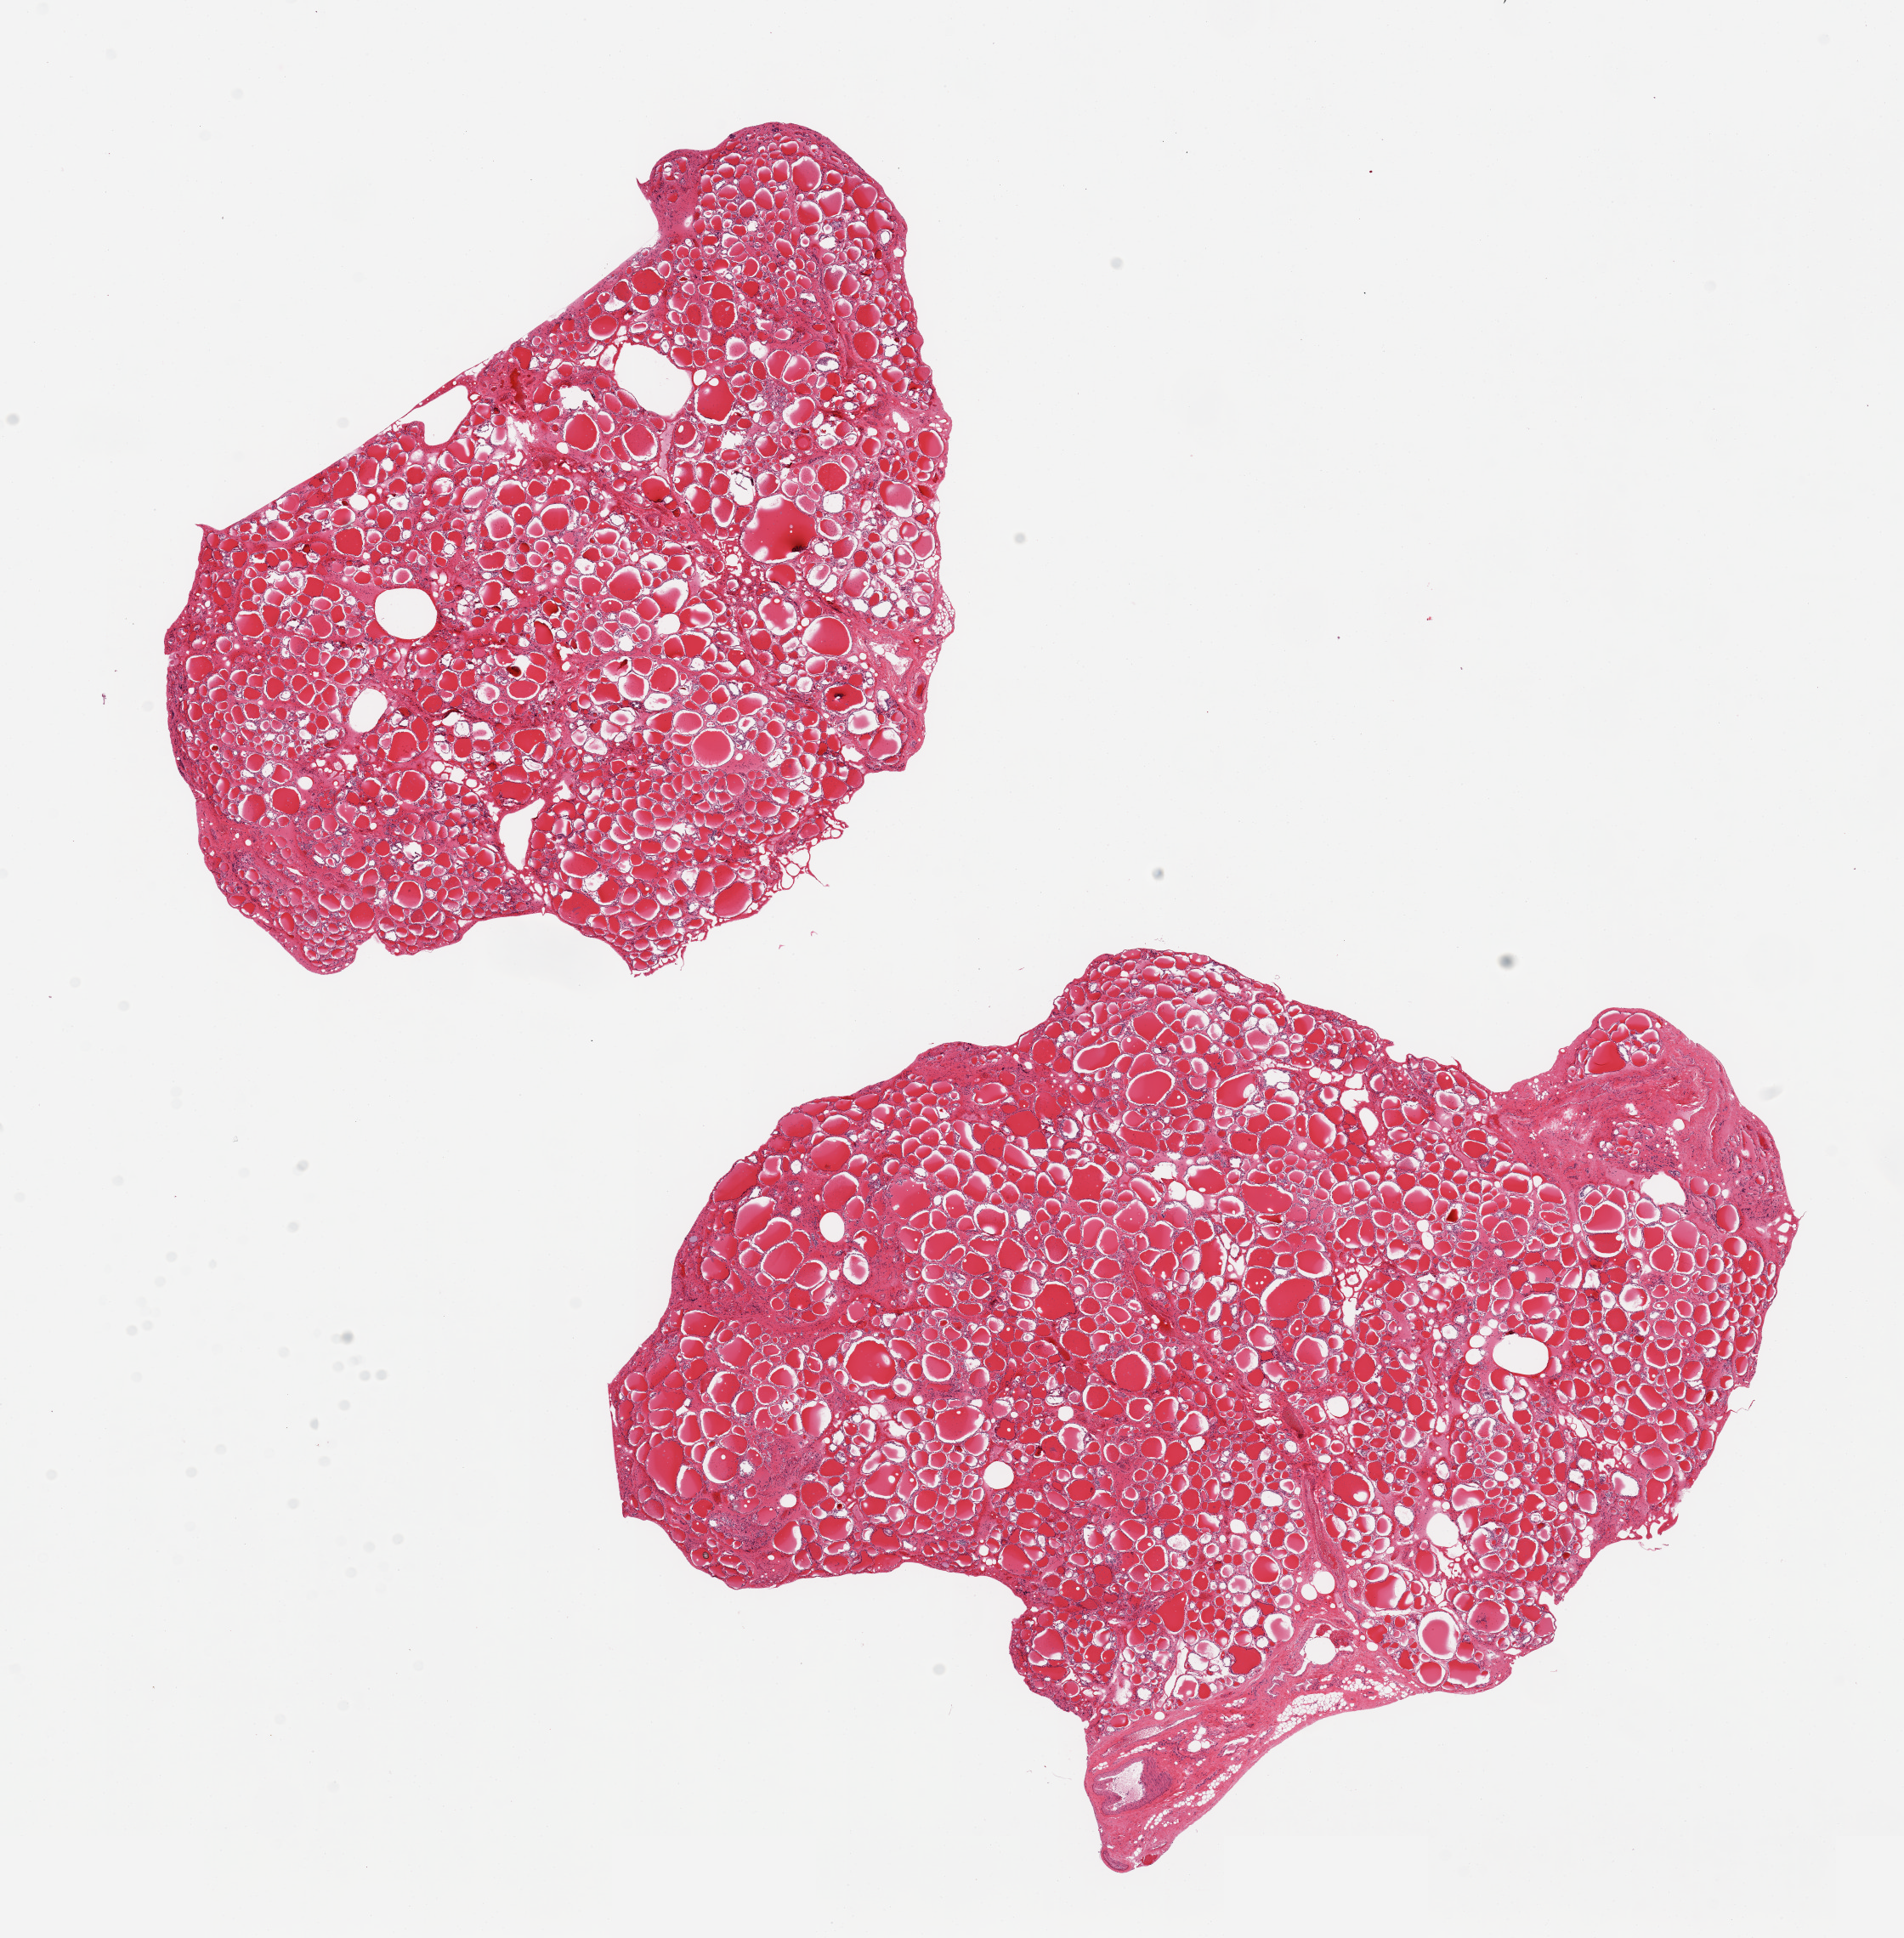
Whole-slide image, haematoxylin and eosin stain — low-resolution overview of the scanned area, about 17.7 x 18.0 mm (acquisition: 20x scan); PAXgene-fixed, paraffin-embedded tissue; target tissue: thyroid; donor tissue sample.
* pathologist's review note for this sample: 2 pieces, no abnormalities